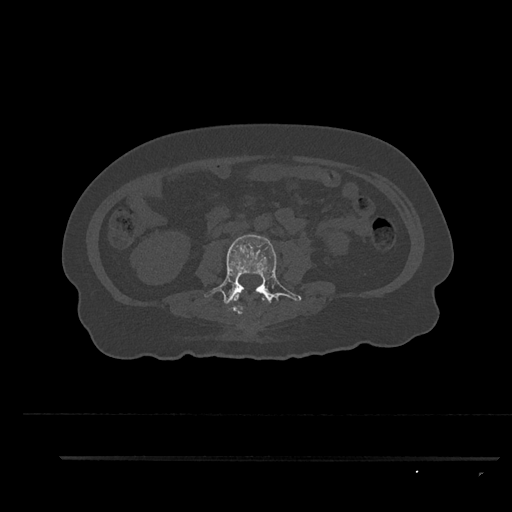
CT including the spine, one axial slice. Position 98 of 797 along the scan axis. Reconstruction kernel Br40s/3. Bone window (W 1800 / L 400 HU). 0.5 mm slice thickness. 512 × 512 image matrix. Patient: female, 44 years. From the clinical record (not read from this slice): primary cancer: renal; vertebrae with lytic lesions (as recorded): L1.
Outlined on this slice (semi-automatically segmented with operator editing):
- L2 vertebra: bounding box [x1, y1, x2, y2] px = [231, 294, 264, 315]
- L3 vertebra: [204, 234, 302, 312]